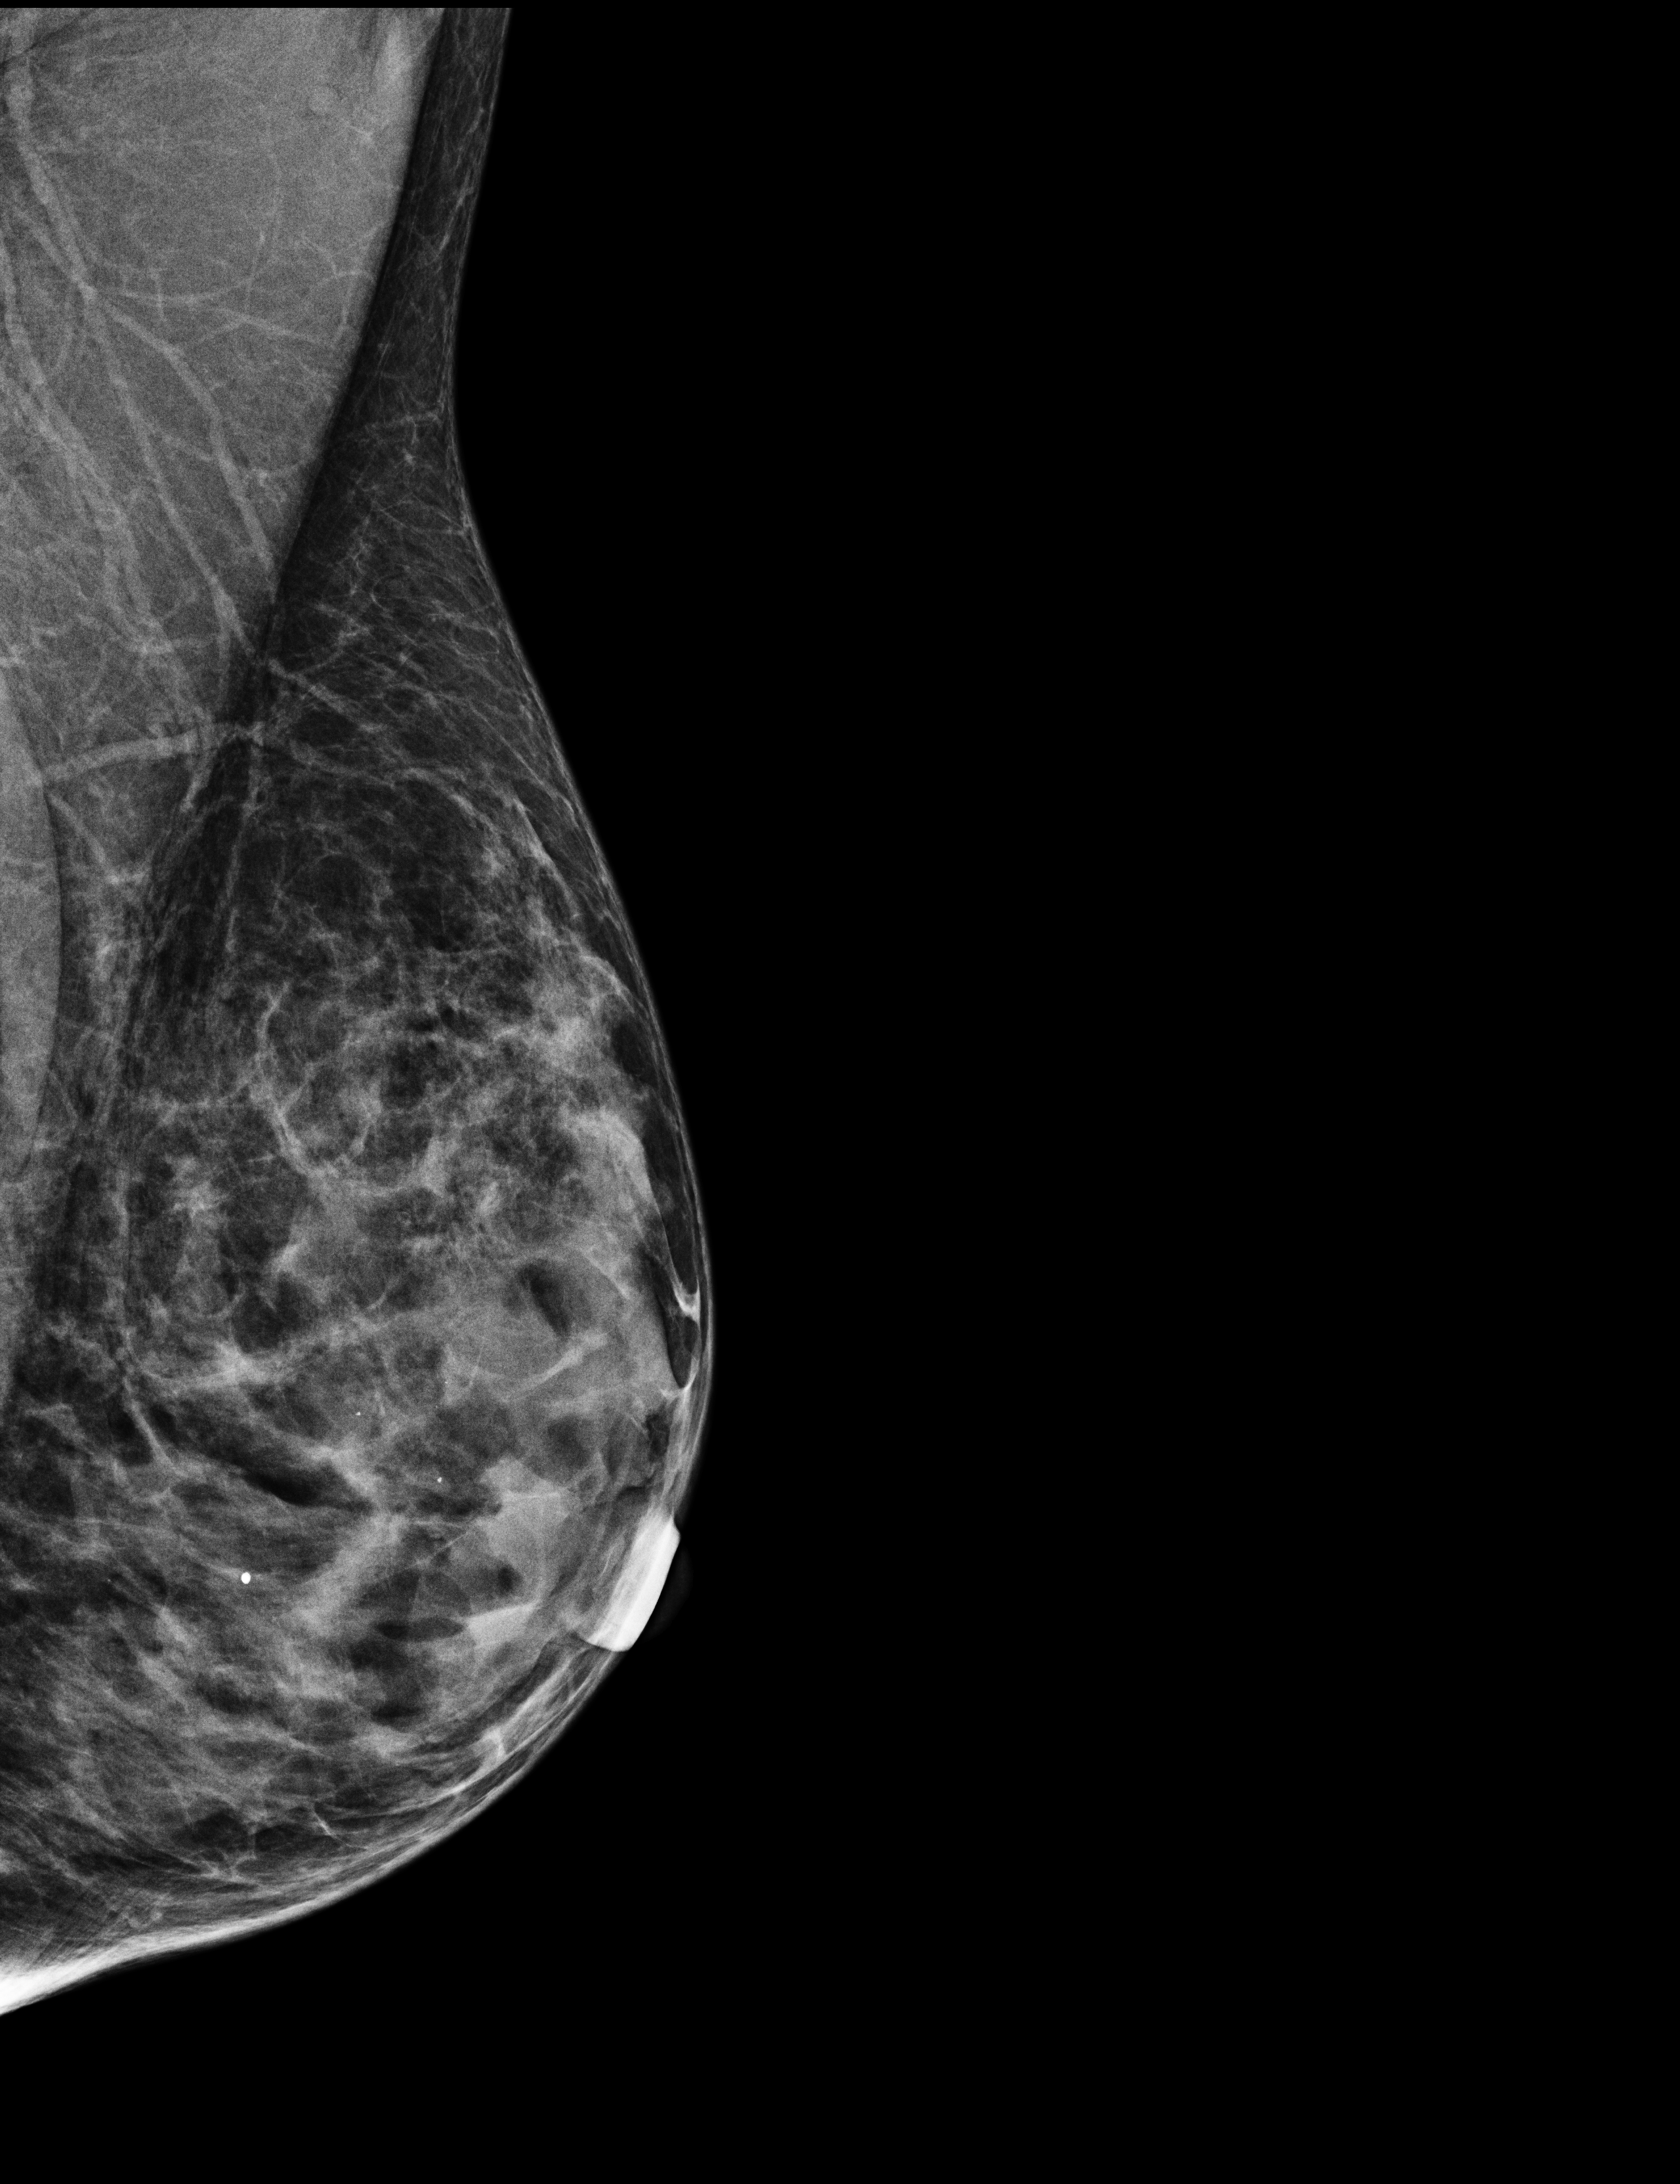
Screening examination, system: Selenia Dimensions. Female patient, age 59 years.
Image type: full-field digital mammogram. Breast: left. Projection: mediolateral oblique (MLO) view.